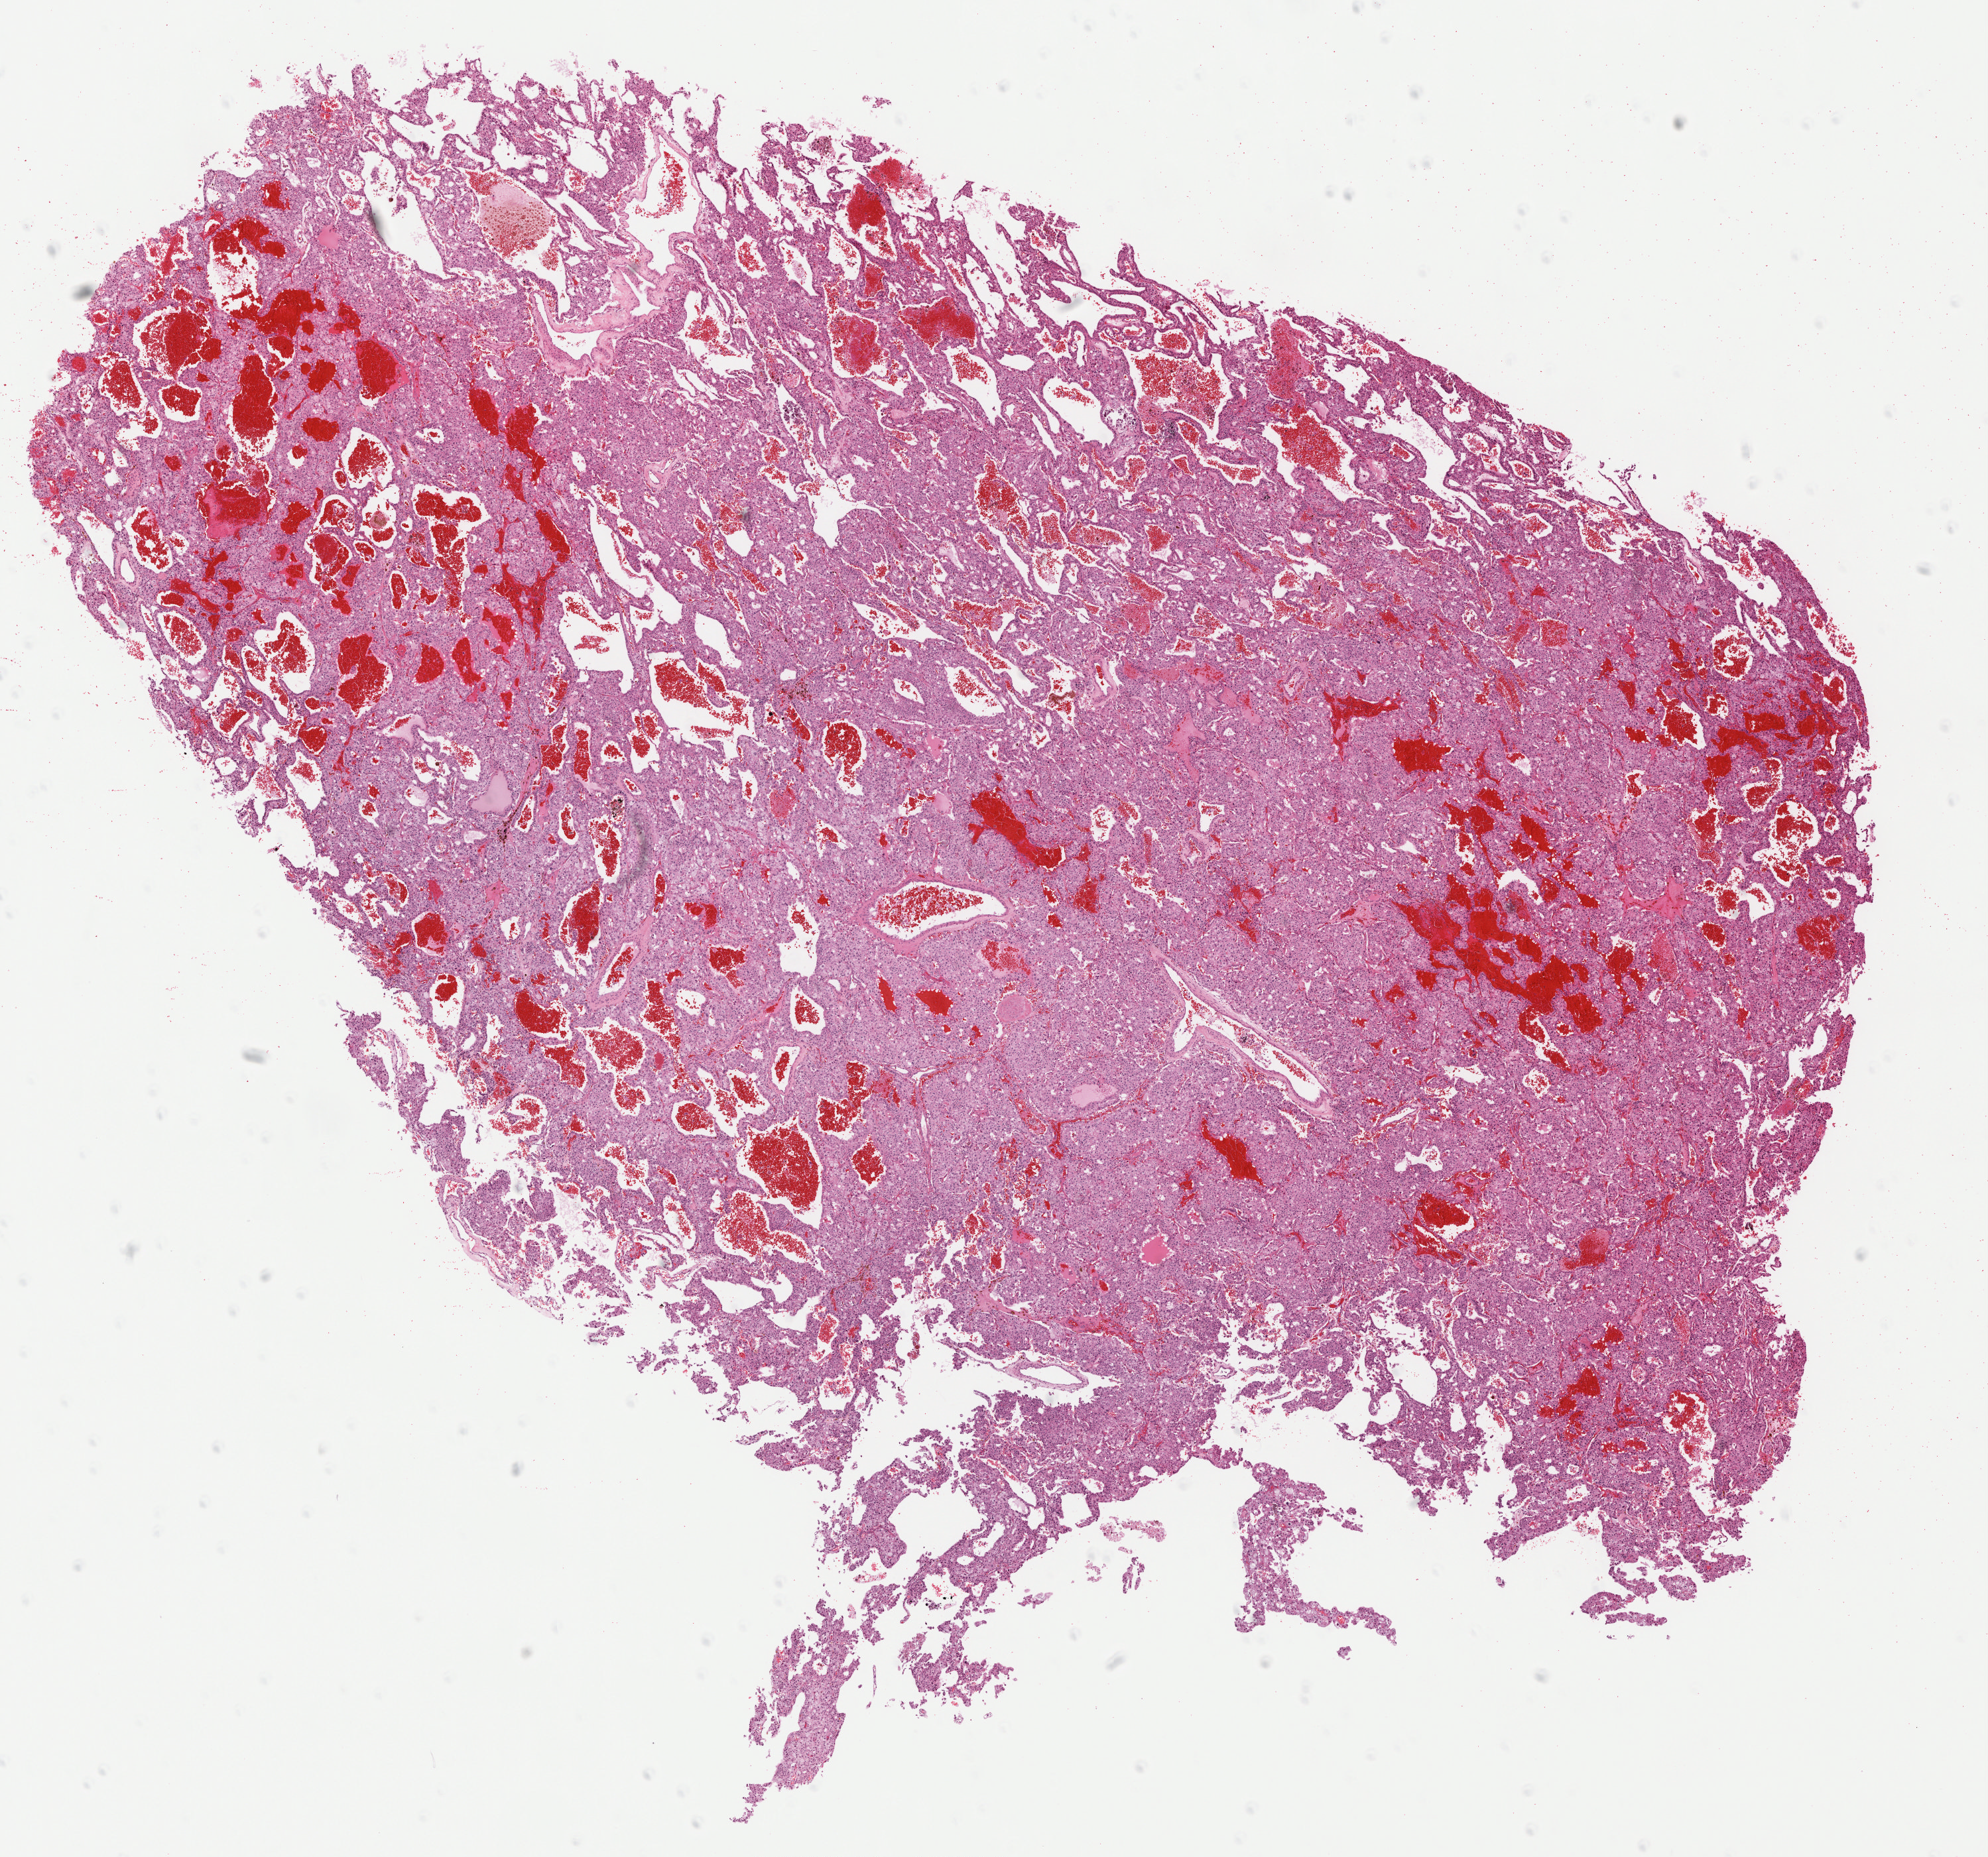
Hematoxylin and eosin (H&E) stained whole-slide image, a low-resolution overview of the entire scanned area, about 12.1 x 11.3 mm, formalin-fixed paraffin-embedded (FFPE) diagnostic section, primary tumour sample from the kidney. Female patient; age at initial diagnosis 65 years.
* AJCC pathologic stage: II (6th edition)
* pathologic diagnosis: Renal cell carcinoma, chromophobe type
* TNM: T2 NX